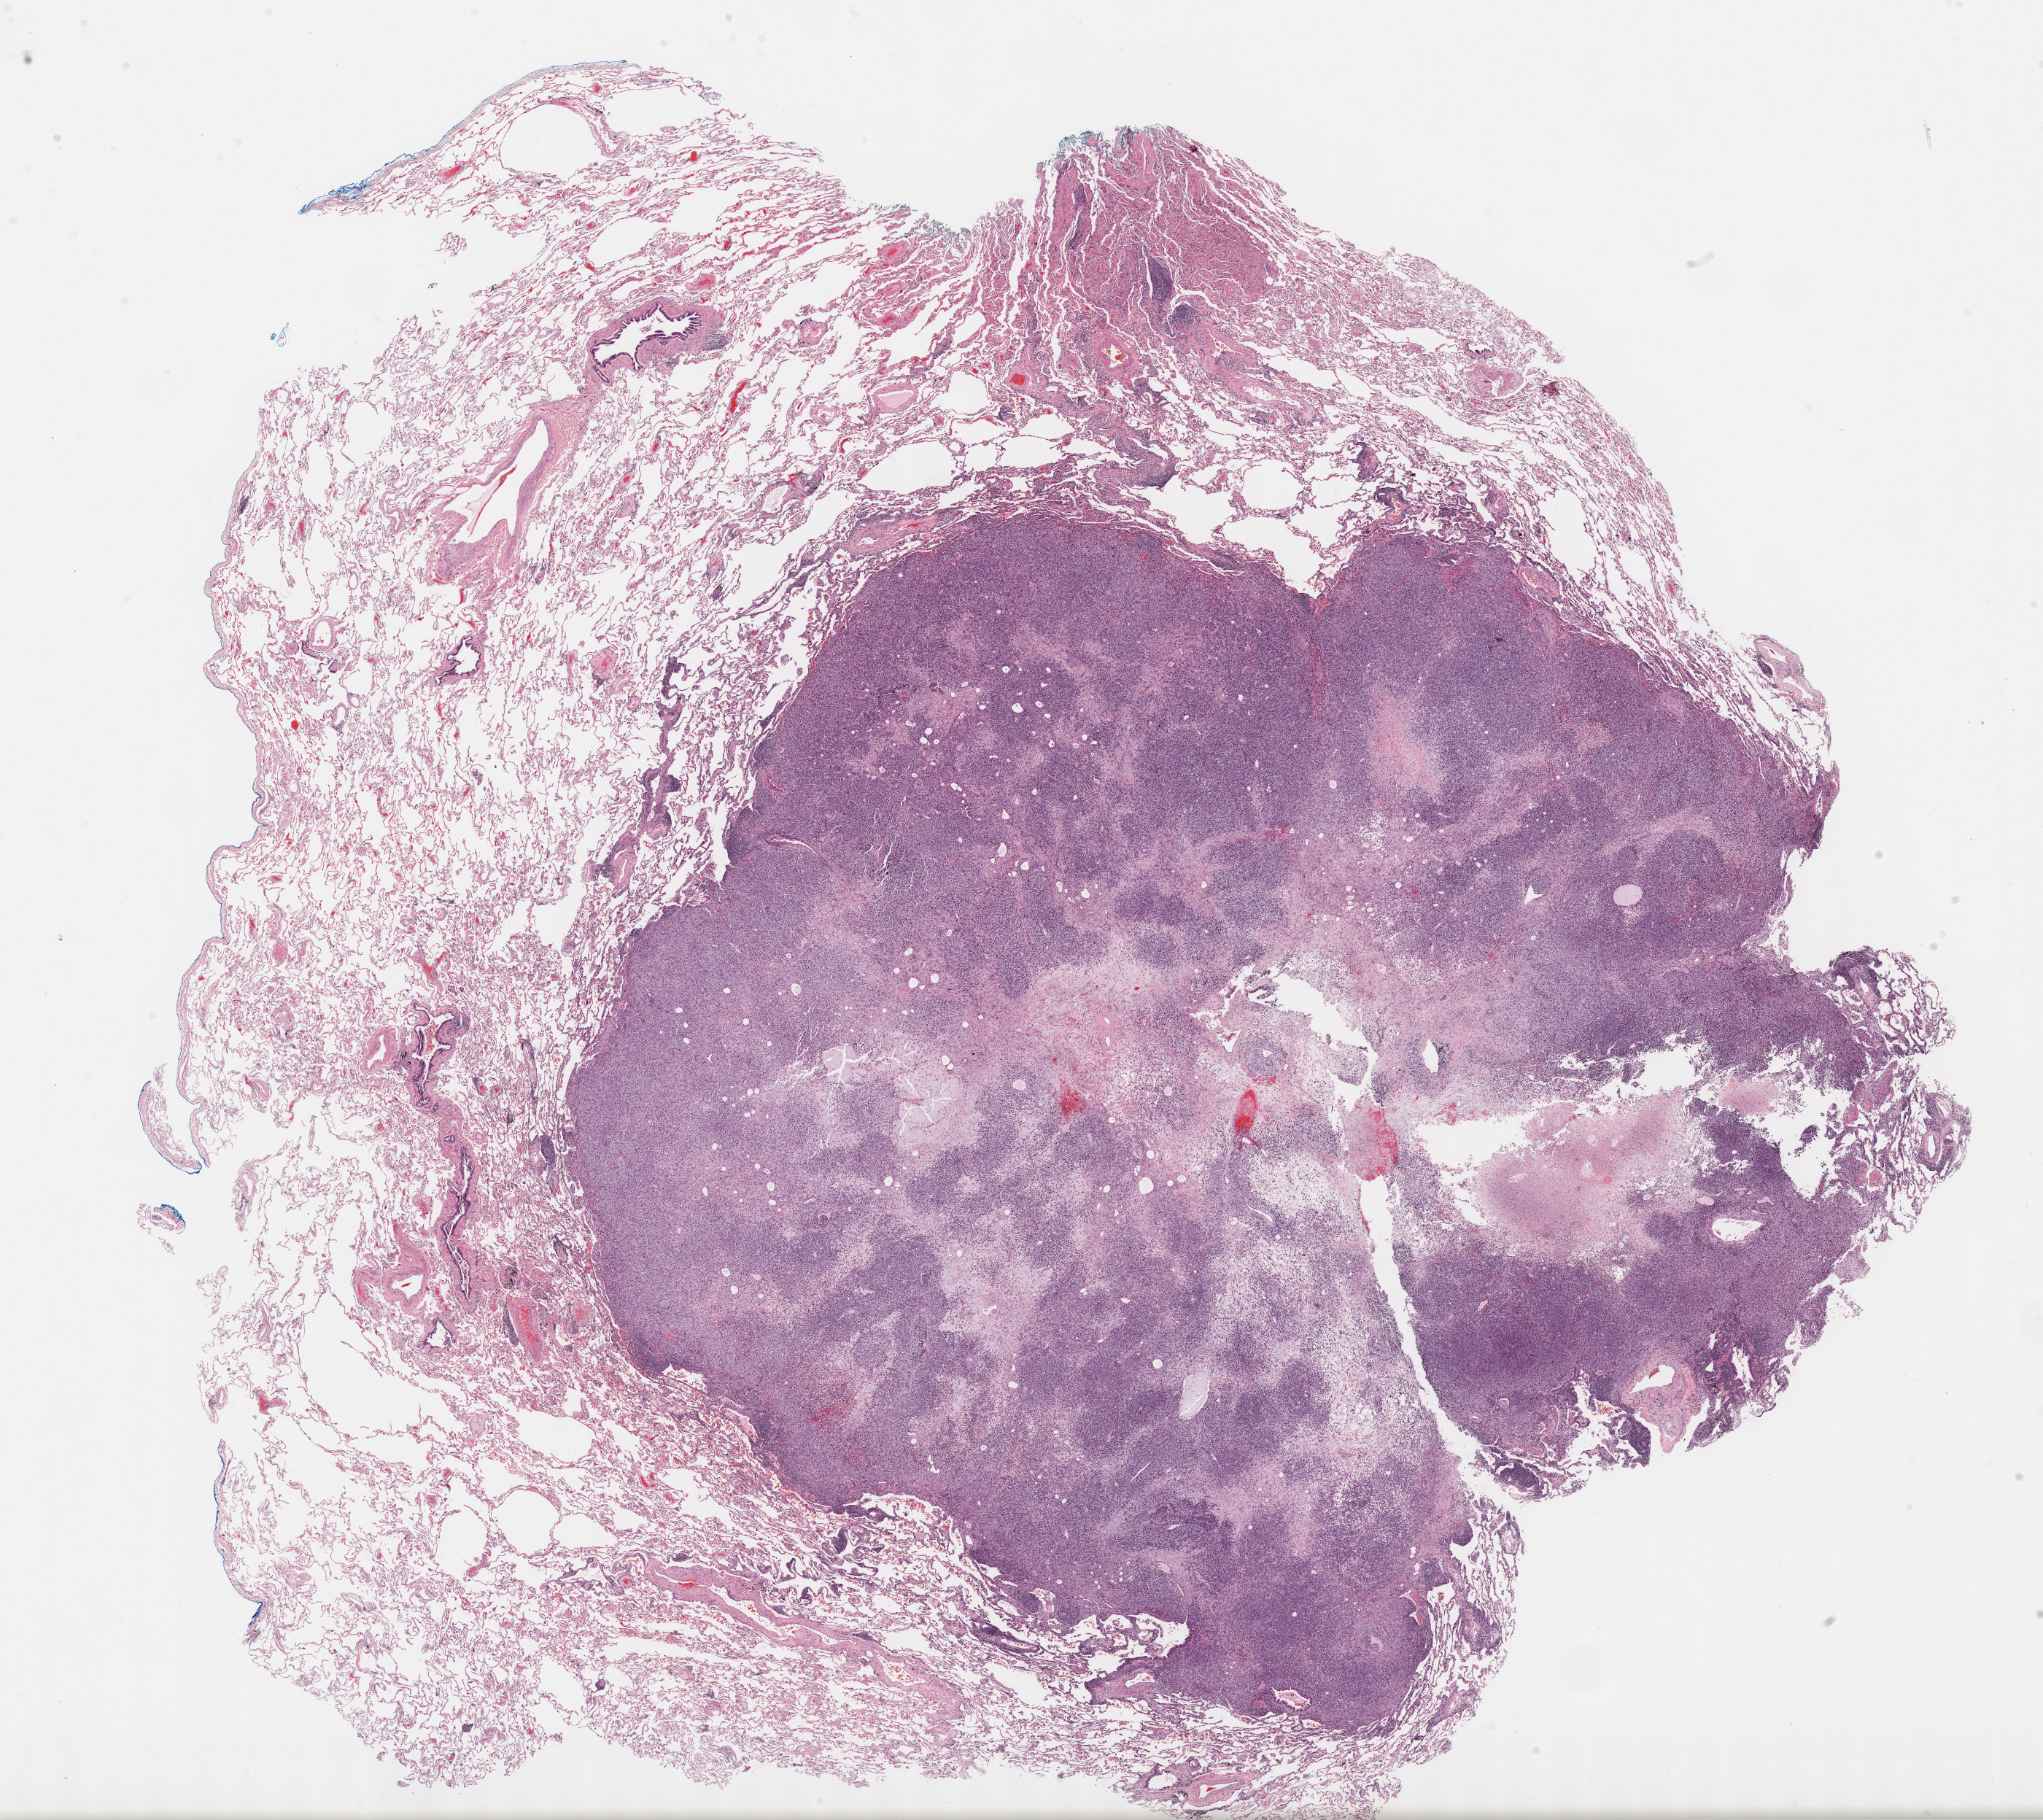
Digitized Hematoxylin and eosin (H&E) stained tissue section (whole slide), shown as a low-resolution overview of the whole scanned area (about 22.7 x 20.2 mm); FFPE section; sample: primary tumour, skin. Male patient; age at initial diagnosis 75 years.
Diagnosis: Malignant melanoma, NOS.